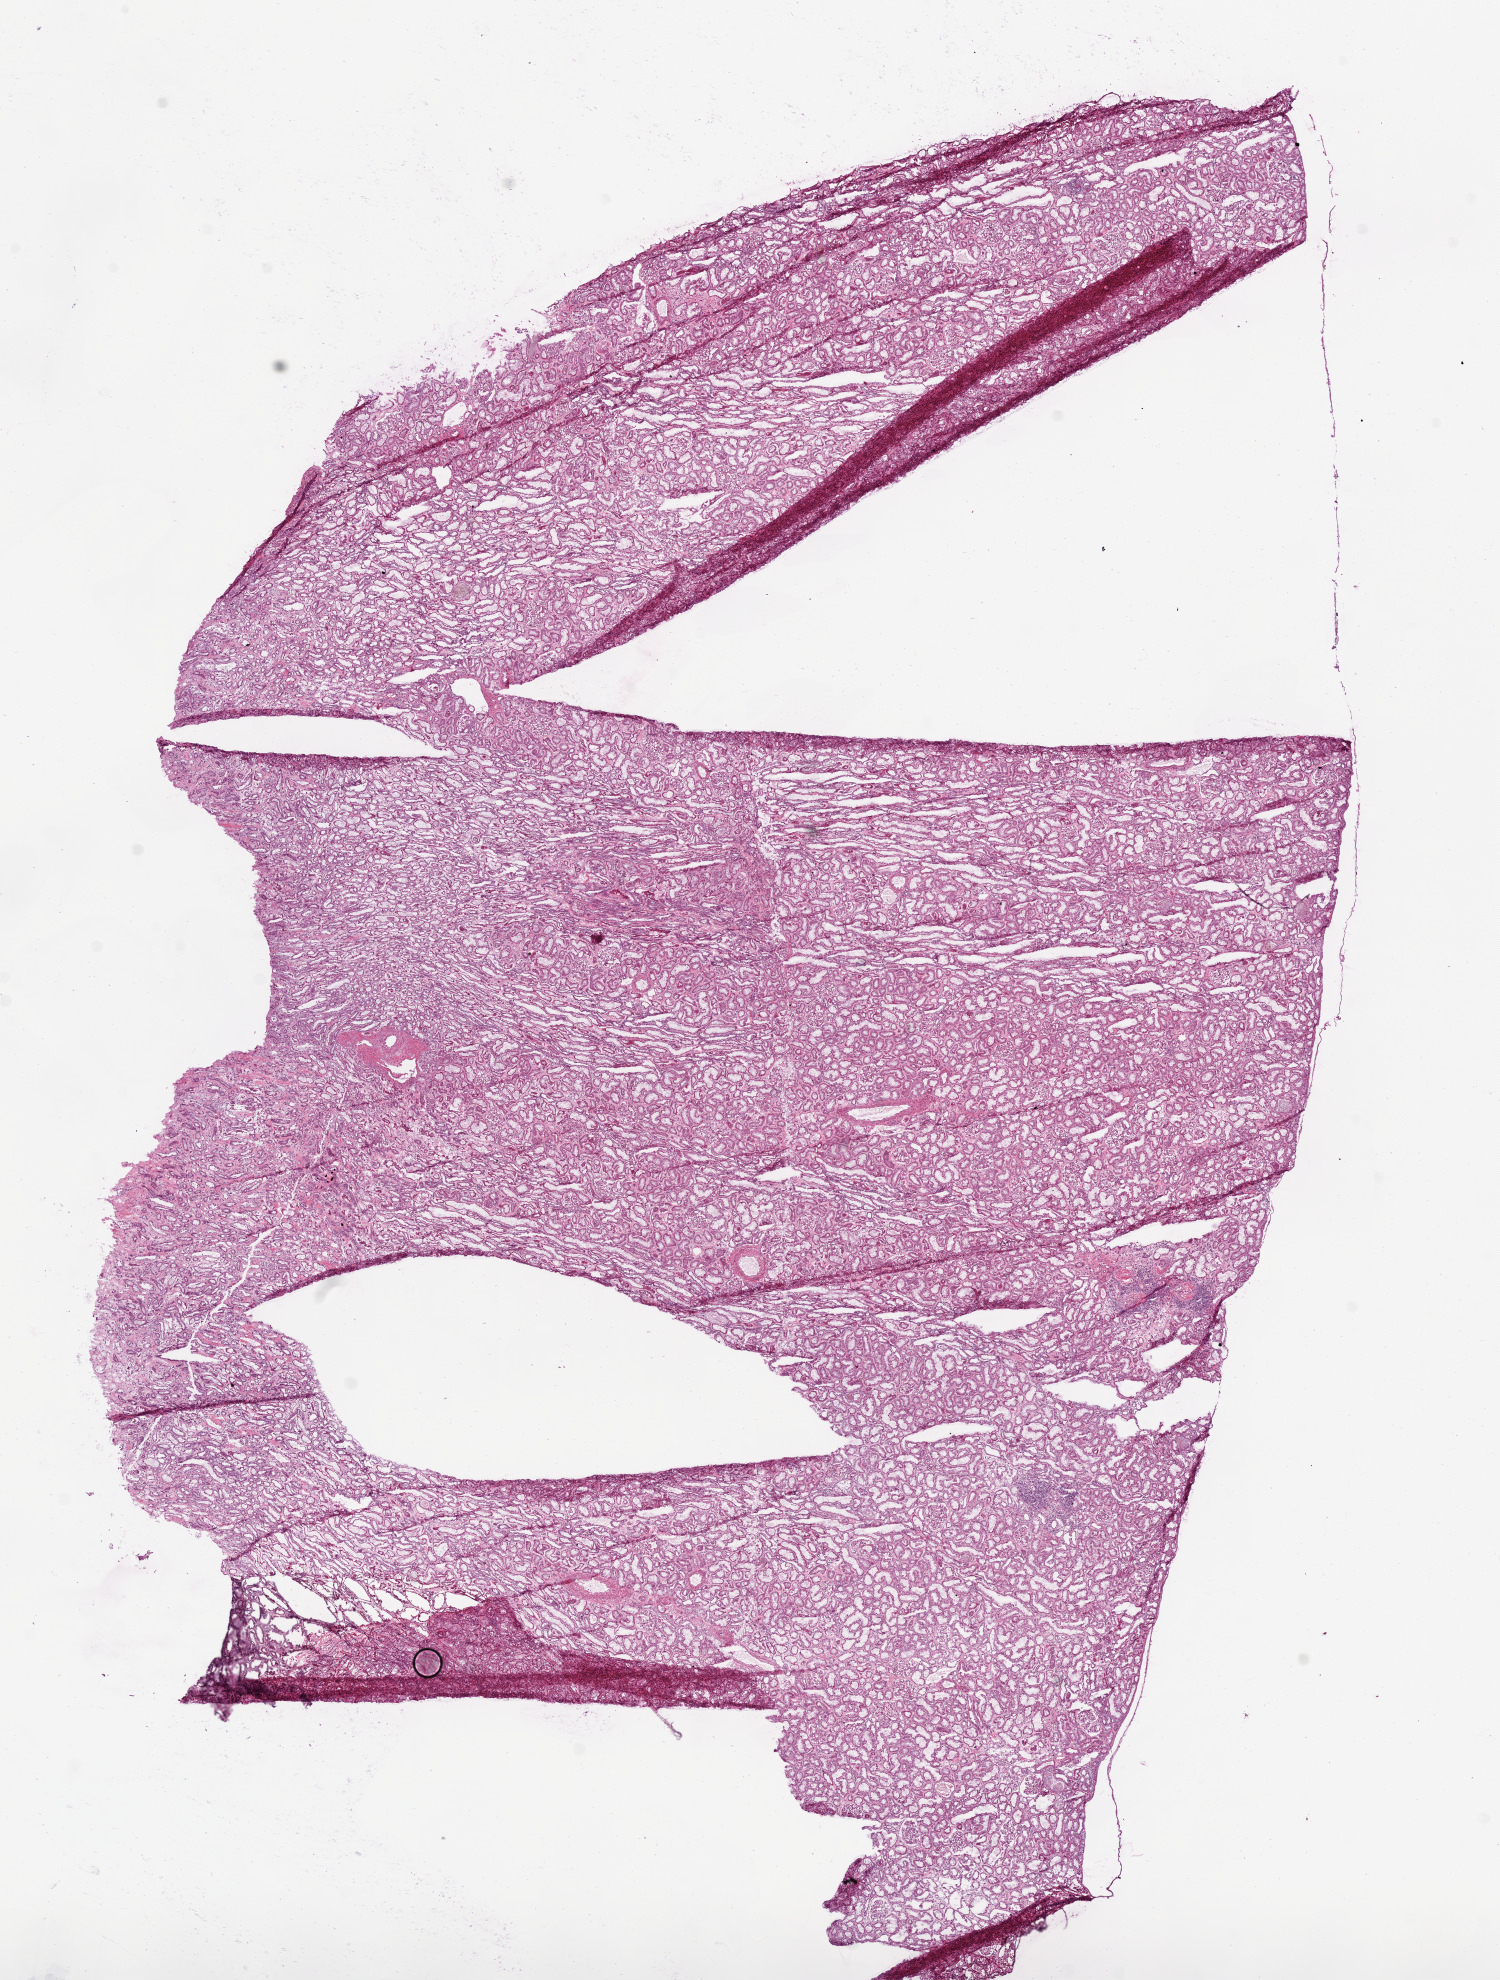
H&E whole-slide image — shown as a low-resolution overview of the whole scanned area (about 12.0 x 15.9 mm). Frozen section from the bottom of the tissue portion. Sample: solid tissue normal (non-tumour tissue), kidney. Male, age 59 years at initial diagnosis.
This section: solid tissue normal sample (biorepository sample class). Patient diagnosis: Clear cell adenocarcinoma, NOS.